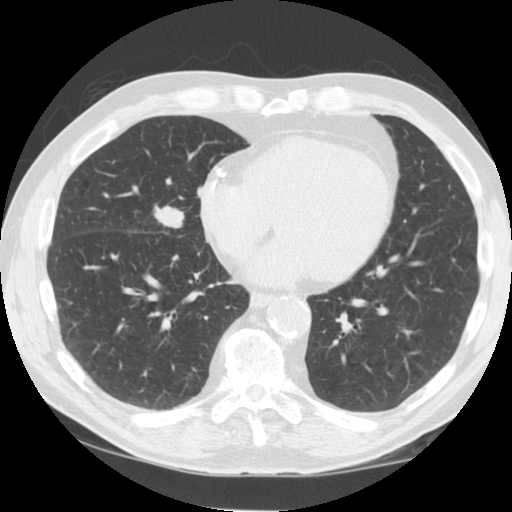
Low-dose screening chest CT, one axial slice. Position 42 of 125 along the scan axis. 120 kVp. Lung window (W 1500 / L -600 HU). 2.5 mm slice thickness. 512 × 512 image matrix, field of view 350 × 350 mm.
Outlined on this slice (outlined manually by an expert reader):
- lesion 1 (tumor, middle lobe of right lung): bounding box (x1, y1, x2, y2) in pixels: (154, 206, 184, 228)